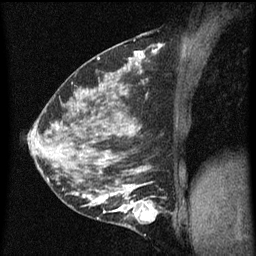
Breast MRI (dynamic contrast-enhanced), one sagittal slice. Slice 28 of 60 in the series (ordered by position). Dynamic contrast-enhanced series, image 2 of 5 at this slice position (ordered by acquisition). 1.5 T. TE 4.2 ms, TR 8 ms. 256 × 256 image matrix, field of view 180 × 180 mm. Female patient, age 35 years.
Annotated regions visible in this slice (semi-automatic segmentation, software-assisted and operator-edited):
- analysis volume of interest (the breast-tissue region the enhancement analysis was run in; not a lesion): bounding box <118,190,165,229> (left, top, right, bottom; pixels)
- tumour enhancement mask (voxels above the 70 % enhancement threshold inside the analysis volume of interest): <118,190,159,221>